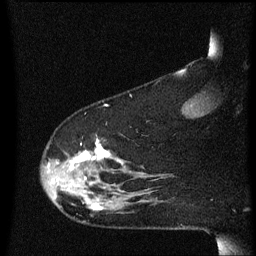
Breast MRI (dynamic contrast-enhanced), one sagittal slice; dynamic contrast-enhanced series, image 2 of 3 at this slice position (ordered by acquisition); 1.5 T; TE 4.2 ms, TR 8.4 ms; 2 mm slice thickness; 256 × 256 image matrix. Patient: female, 48 years.
Outlined on this slice (semi-automatic segmentation, software-assisted and operator-edited):
- analysis volume of interest (the breast-tissue region the enhancement analysis was run in; not a lesion): bounding box [x1, y1, x2, y2] px = [41, 140, 134, 211]
- tumour enhancement mask (voxels above the 70 % enhancement threshold inside the analysis volume of interest): [69, 140, 110, 211]